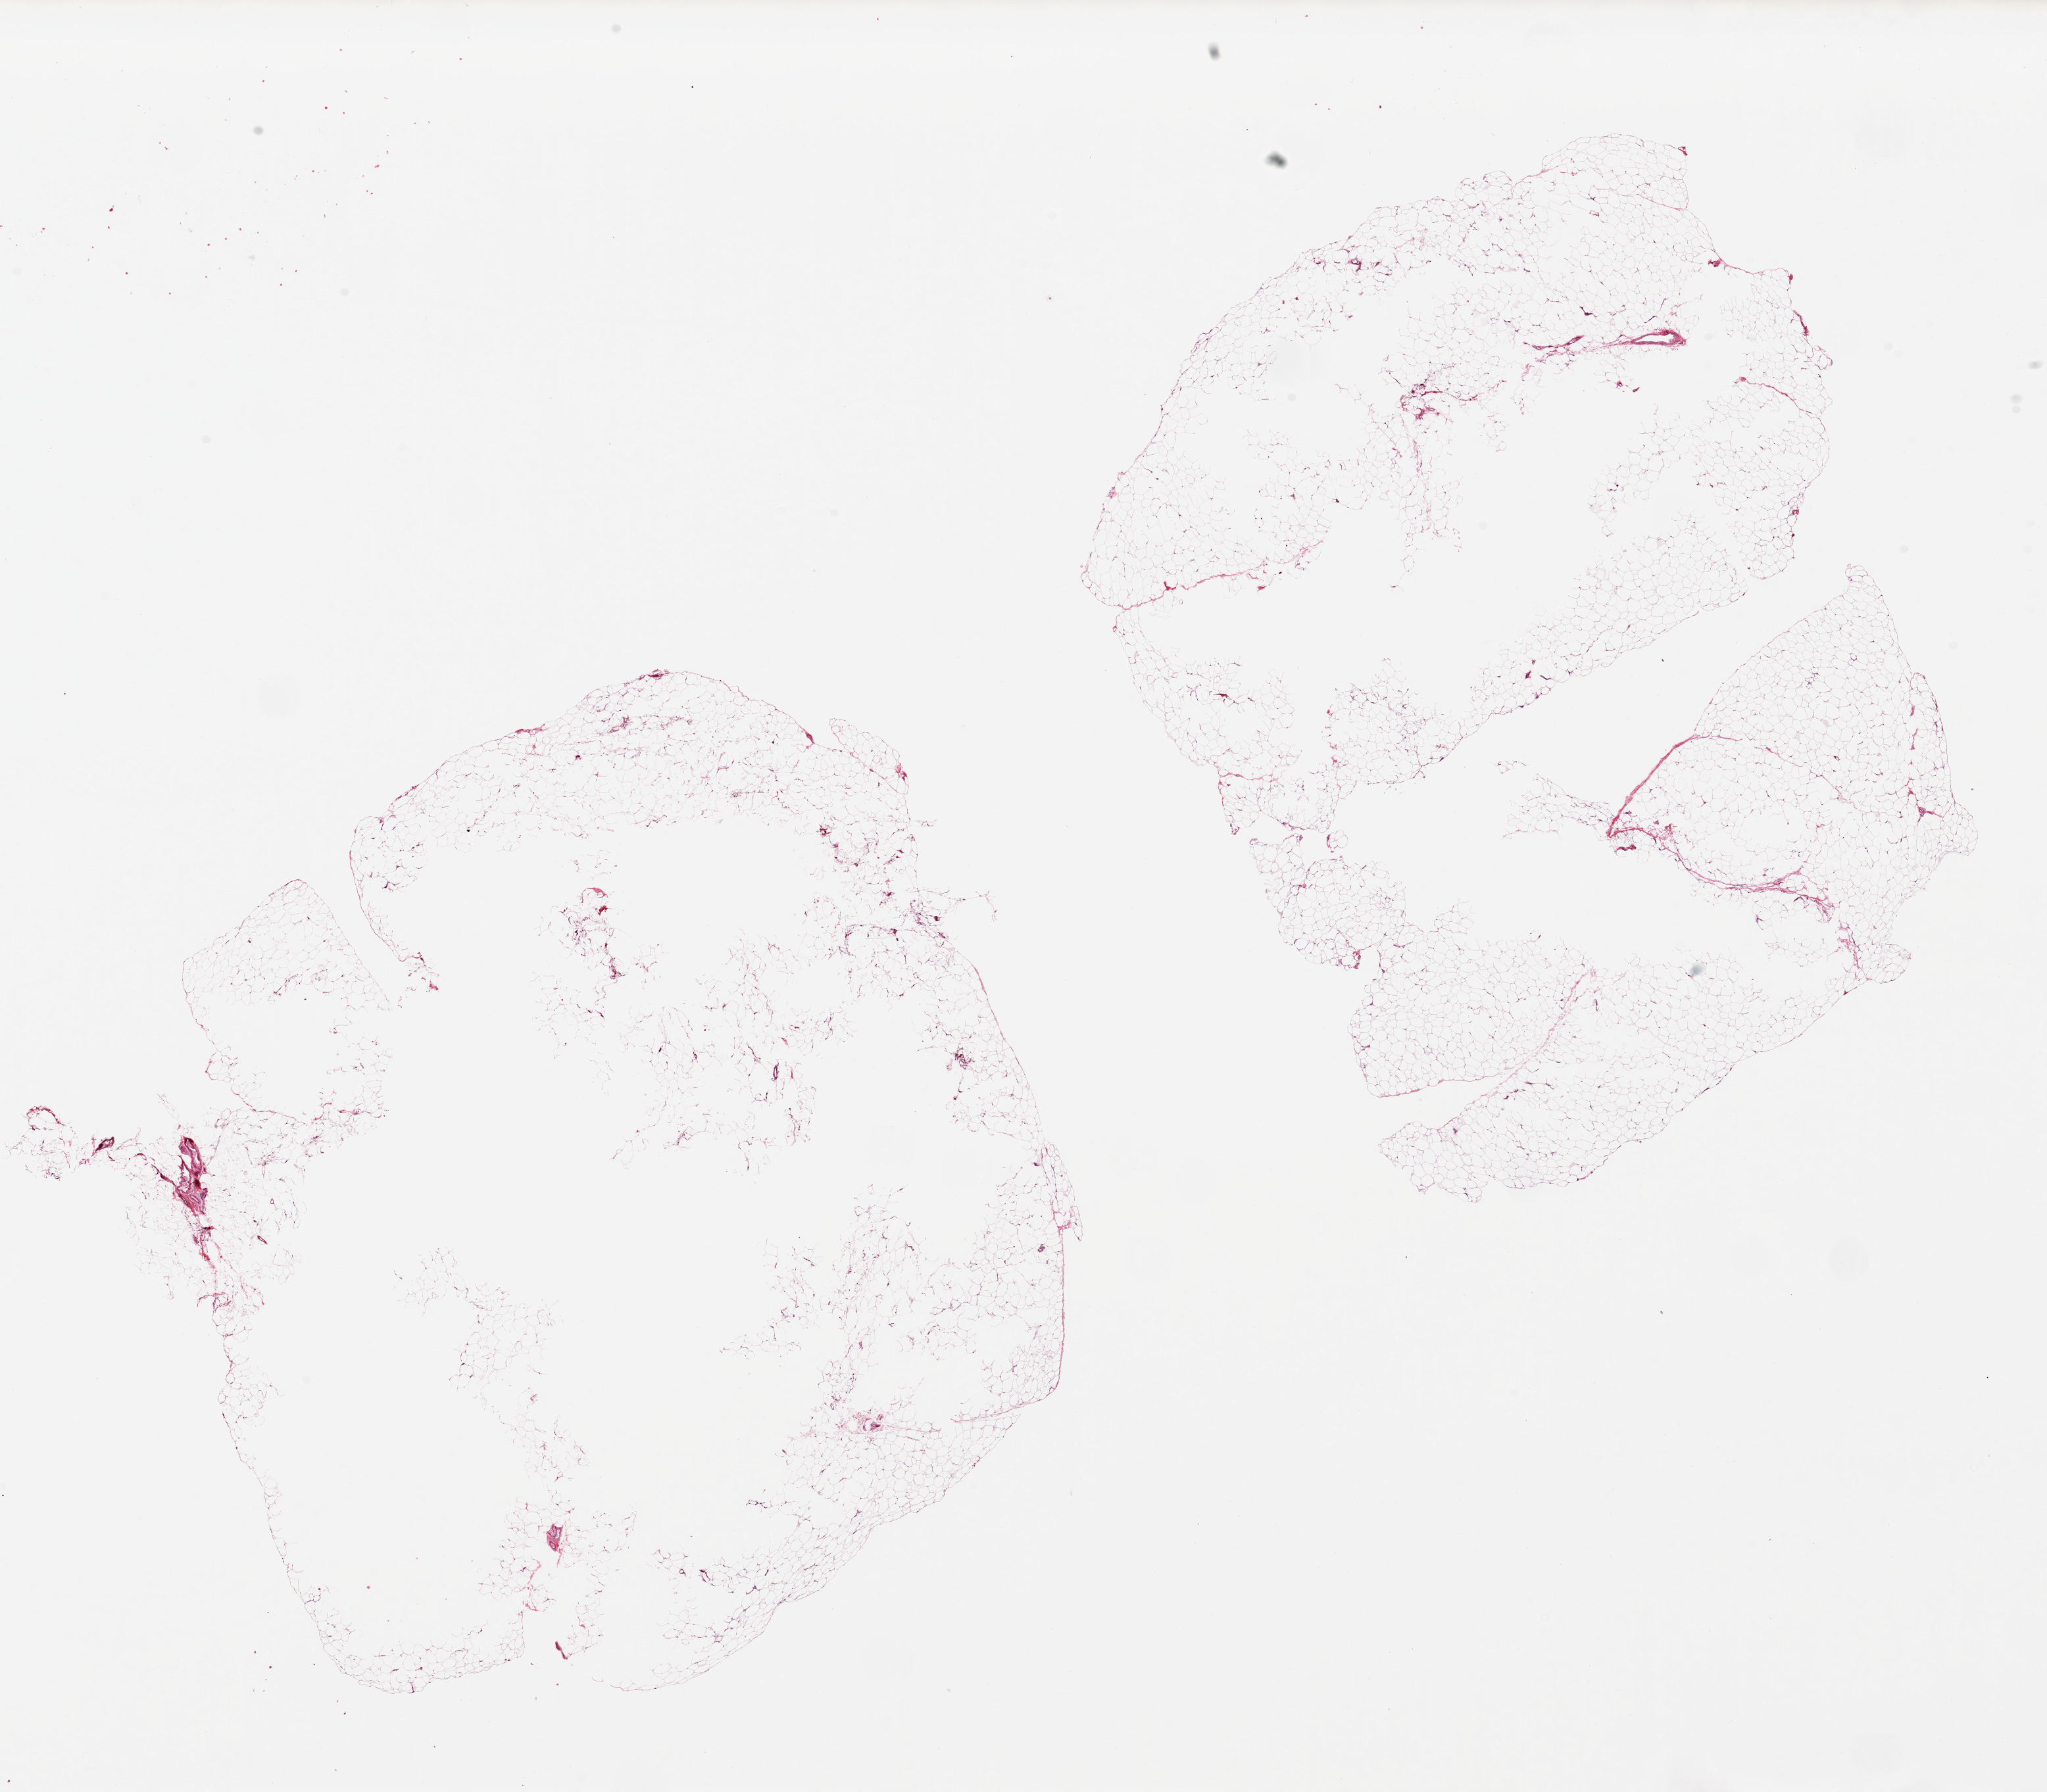
H&E whole-slide image, brightfield, a low-resolution overview of the entire scanned area, about 24.6 x 21.6 mm (acquisition: 20x scan), PAXgene-fixed, paraffin-embedded tissue, target tissue: adipose tissue, donor tissue sample. Donor sex: male.
Review note (as recorded): 2 pieces ~12x10mm.